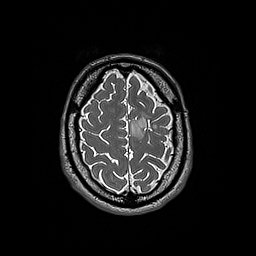
Brain MRI from a brain-tumour surgery series, one axial slice. Slice 48 of 192 in the series (ordered by position). 256 × 256 image matrix. Case-level facts recorded for this patient, not image findings: histopathology: Oligodendroglioma; WHO grade: 3; IDH mutation: yes; tumour location: Left Frontal.
Annotated regions visible in this slice (manually delineated by an expert):
- tumour: bounding box <130,113,157,139> (left, top, right, bottom; pixels)